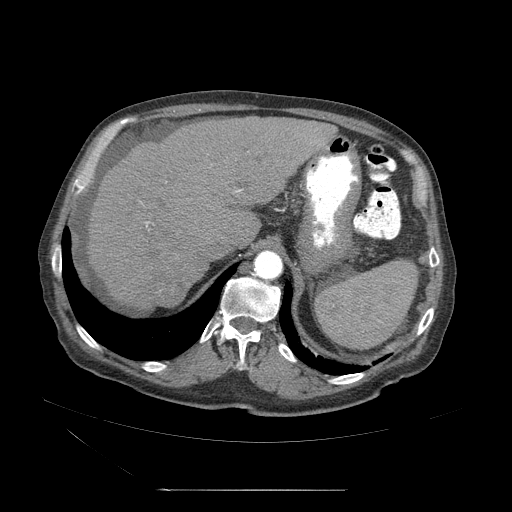
Contrast-enhanced abdominal CT (liver protocol), one axial slice; position 37 of 71 along the scan axis; reconstruction kernel STANDARD; 120 kVp; soft-tissue window (W 400 / L 40 HU); 512 × 512 image matrix, field of view 440 × 440 mm. Case-level facts recorded for this patient, not image findings: diagnosis: hepatocellular carcinoma (patient treated with transarterial chemoembolisation; whether this scan precedes or follows treatment is not stated here); TNM stage (as recorded): Stage-II; Child-Pugh class: A; tumour nodularity: multinodular; tumour size: 1 cm.
Annotated regions visible in this slice (semi-automatic segmentation, software-assisted and operator-edited):
- abdominal aorta: bounding box <253,251,283,280> (left, top, right, bottom; pixels)
- liver parenchyma outside the tumour (the mass and vessels are separate outlines, so this box may not span the whole liver): <80,117,338,317>
- mass: <161,286,182,311>
- liver vessels: <134,161,234,289>